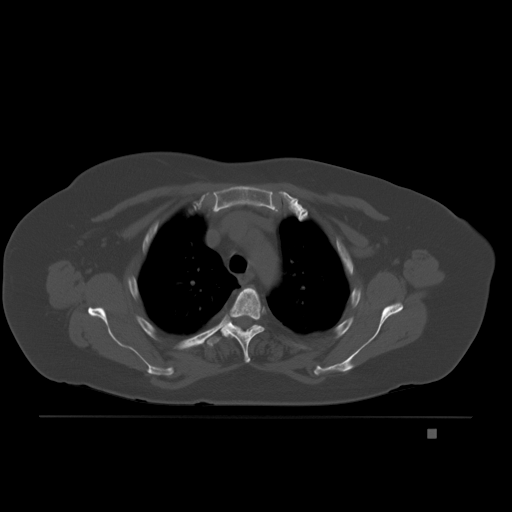
CT including the spine, one axial slice; position 158 of 221 along the scan axis; bone window (W 1800 / L 400 HU); 3 mm slice thickness; 512 × 512 image matrix, field of view 474 × 474 mm. Female patient, age 63 years. From the clinical record (not read from this slice): primary cancer: breast.
Structures marked on this image (semi-automatically segmented with operator editing):
- T3 vertebra: bounding box (x1, y1, x2, y2) in pixels: (220, 288, 265, 362)
- T4 vertebra: (207, 322, 258, 347)